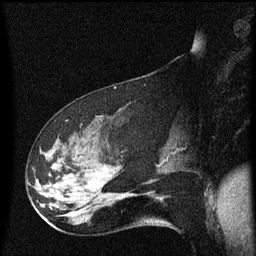
Breast MRI (dynamic contrast-enhanced), one sagittal slice. Slice 26 of 60 in the series (ordered by position). Dynamic contrast-enhanced series, image 2 of 3 at this slice position (ordered by acquisition). 1.5 T. TE 4.2 ms, TR 8.4 ms. 2 mm slice thickness. 256 × 256 image matrix. Patient: female, 48 years.
Annotated regions visible in this slice (semi-automatic segmentation, software-assisted and operator-edited):
- analysis volume of interest (the breast-tissue region the enhancement analysis was run in; not a lesion): bounding box <31,116,134,225> (left, top, right, bottom; pixels)
- tumour enhancement mask (voxels above the 70 % enhancement threshold inside the analysis volume of interest): <42,204,44,207>